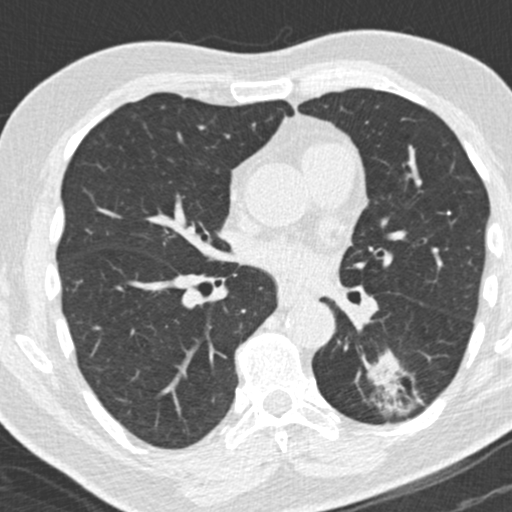
Low-dose screening chest CT, axial slice. Third screening round (two years after baseline). Lung window (W 1500 / L -600 HU). Male participant, aged 66 years at enrolment. Former smoker at enrolment.
• Expert reader's lesion annotation, bounding box <357,353,426,426> (left, top, right, bottom; pixels).
• The exam's reader record, not a measurement of the box and not confirmed to be the same lesion: non-calcified nodule or mass ≥4 mm, left lower lobe, 31 × 24 mm, spiculated (stellate) margins, pre-existing on the prior screen: yes; interval growth: yes.
• Official screen result: positive, other.
• Participant outcome: lung cancer diagnosed 56 days after this screen — adenocarcinoma, NOS, left lower lobe, poorly differentiated (G3), stage IB (AJCC 6th edition), 38 mm at pathology.